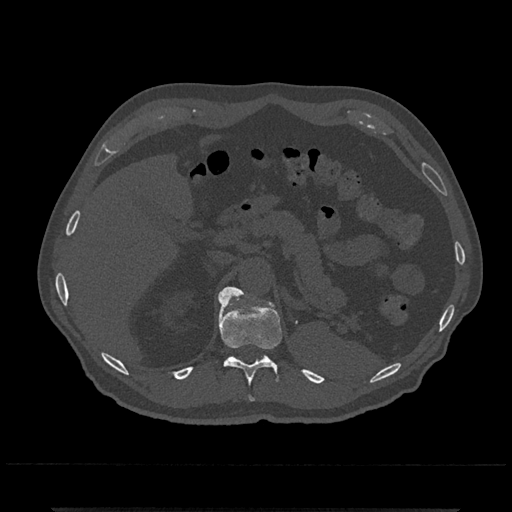
CT including the spine, one axial slice. Slice 480 of 797 in the series (ordered by position). 120 kVp. Bone window (W 1800 / L 400 HU). 0.5 mm slice thickness. 512 × 512 image matrix. Patient: male, 67 years. From the clinical record (not read from this slice): primary cancer: prostate.
Structures marked on this image (semi-automatically segmented with operator editing):
- T11 vertebra: bounding box [x1, y1, x2, y2] px = [218, 293, 282, 402]
- T12 vertebra: [220, 286, 246, 305]